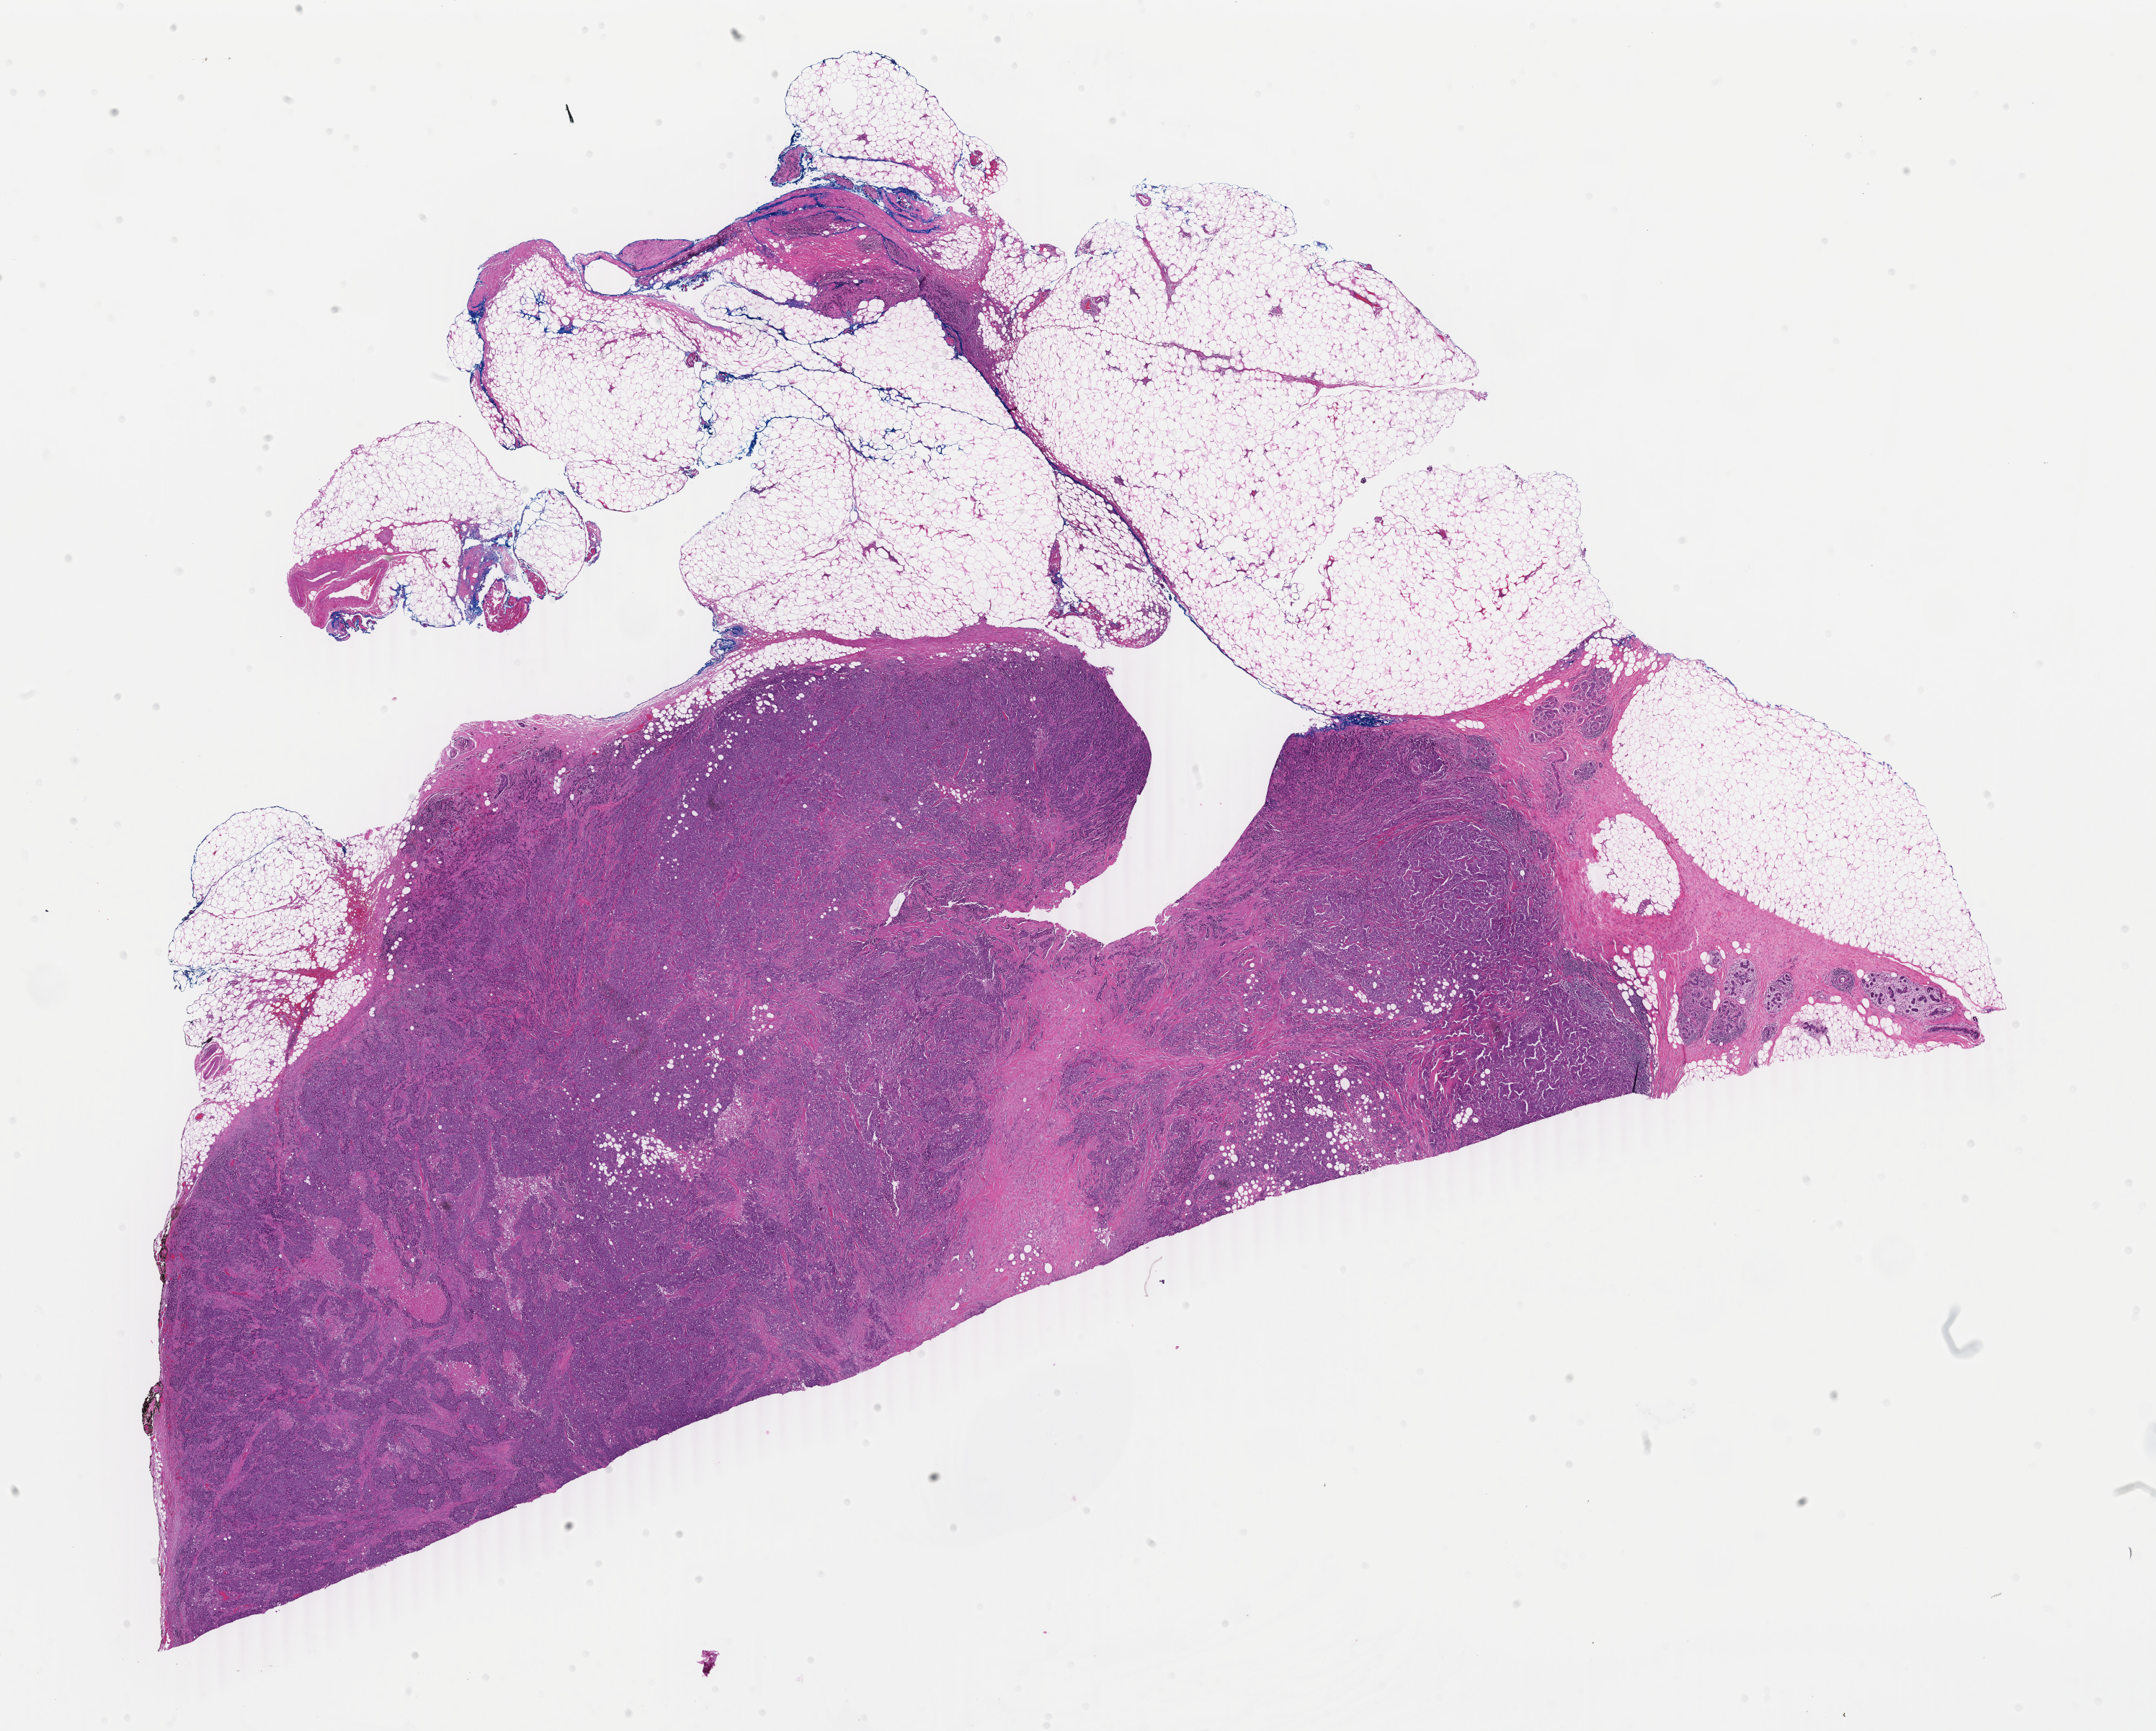
Whole-slide histology image, Hematoxylin and eosin (H&E) stained — low-resolution overview of the scanned area, about 23.8 x 19.1 mm (from a 40x scan); formalin-fixed paraffin-embedded (FFPE) diagnostic section; sample: primary tumour, breast. Patient: female, age at initial diagnosis 40 years.
AJCC pathologic stage: IIA (6th edition). Diagnosis: Infiltrating duct carcinoma, NOS.